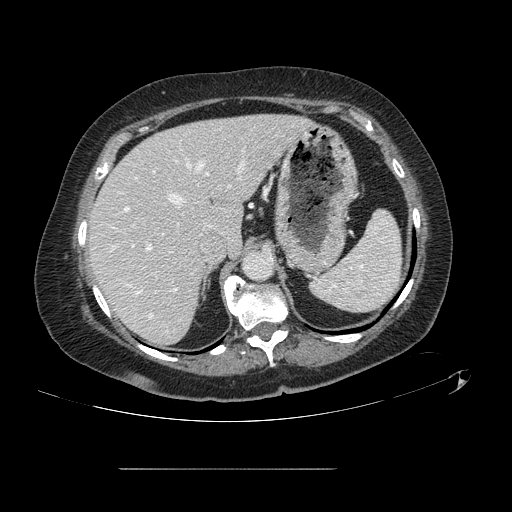
Contrast-enhanced abdominal CT, one axial slice. Position 94 of 148 along the scan axis. 120 kVp. Soft-tissue window (W 400 / L 40 HU). 2.5 mm slice thickness. 512 × 512 image matrix, field of view 439 × 439 mm. Female patient, age 75 years. Case-level facts recorded for this patient, not image findings: diagnosis: colorectal cancer liver metastases, imaged before liver resection; multiple liver metastases: no; largest metastasis: 2.4 cm; disease in both lobes: no.
Outlined on this slice (expert manual segmentation):
- hepatic veins: bounding box (x1, y1, x2, y2) in pixels: (129, 163, 245, 317)
- liver: (90, 115, 309, 345)
- planned liver remnant (the part of the liver to remain after resection): (90, 115, 309, 345)
- portal vein (with intrahepatic branches): (125, 149, 246, 291)